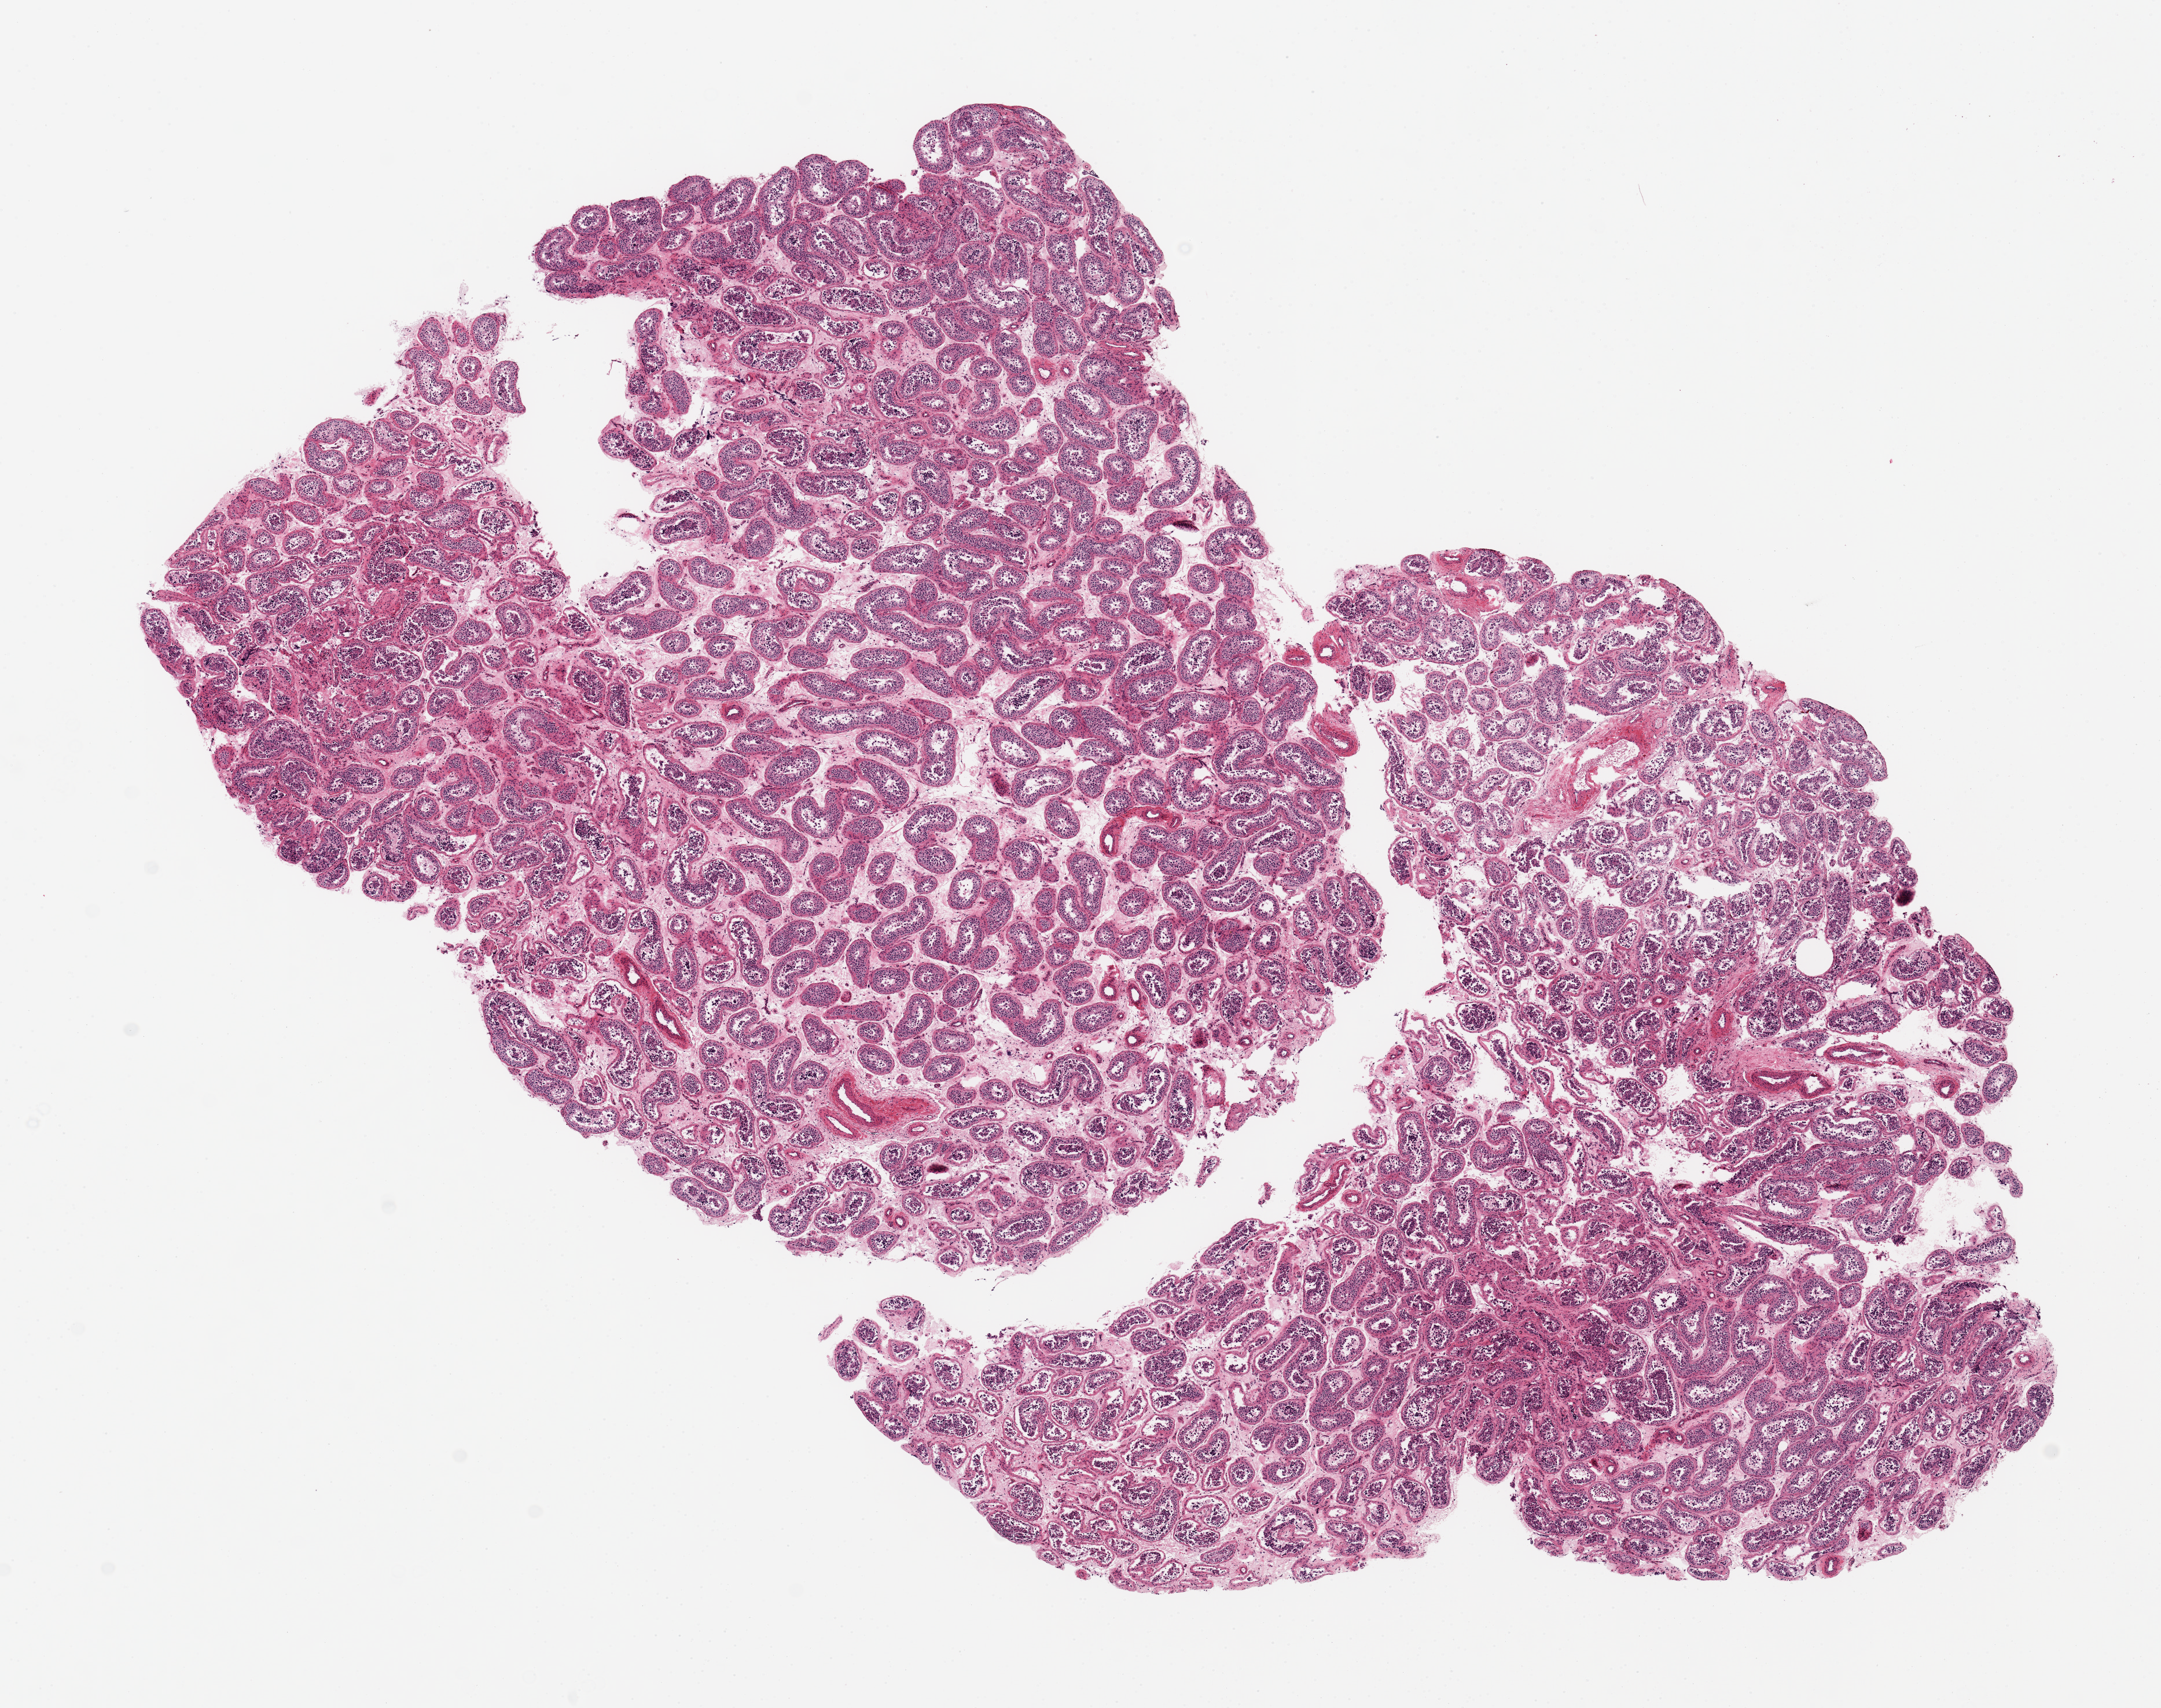
Digitized H&E-stained section — shown as a low-resolution overview of the whole scanned area (about 14.8 x 11.7 mm, from a 20x scan). PAXgene-fixed paraffin-embedded (PFPE) section. Section of testis (target tissue). Tissue donor sample. Donor sex: male.
Review note (as recorded): 11x6.4mm, slightly fragmented, well preserved.